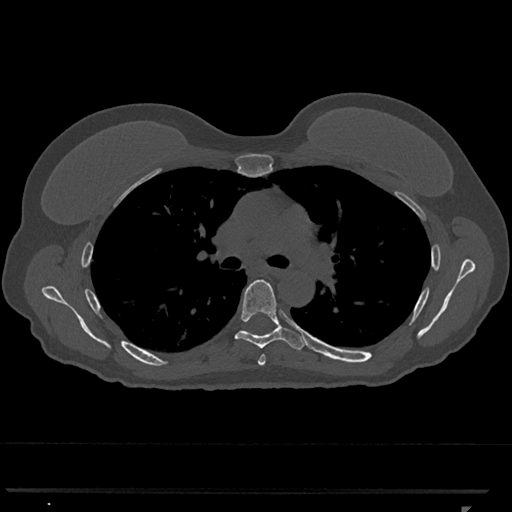
CT including the spine, one axial slice; position 764 of 793 along the scan axis; 120 kVp; bone window (W 1800 / L 400 HU); 512 × 512 image matrix, field of view 380 × 380 mm. Female patient, age 62 years. From the clinical record (not read from this slice): primary cancer: renal.
Annotated regions visible in this slice (semi-automatically segmented with operator editing):
- T5 vertebra: bounding box [x1, y1, x2, y2] px = [258, 354, 266, 366]
- T6 vertebra: [235, 279, 306, 350]